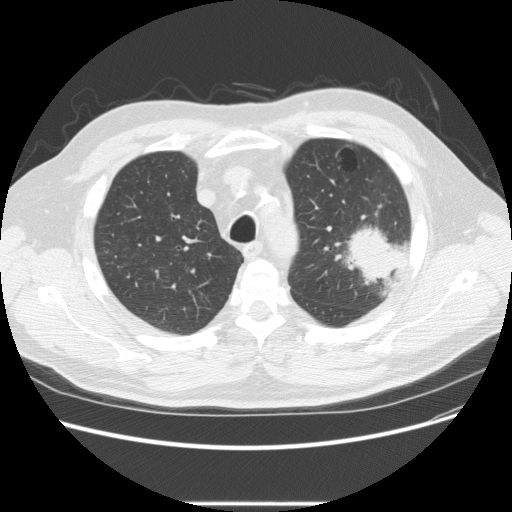
Low-dose screening chest CT, one axial slice; lung window (W 1500 / L -600 HU); 2.5 mm slice thickness; 512 × 512 image matrix, field of view 380 × 380 mm.
Outlined on this slice (manually delineated by an expert):
- lesion 1 (tumor, upper lobe of left lung): bounding box <345,226,401,288> (left, top, right, bottom; pixels)